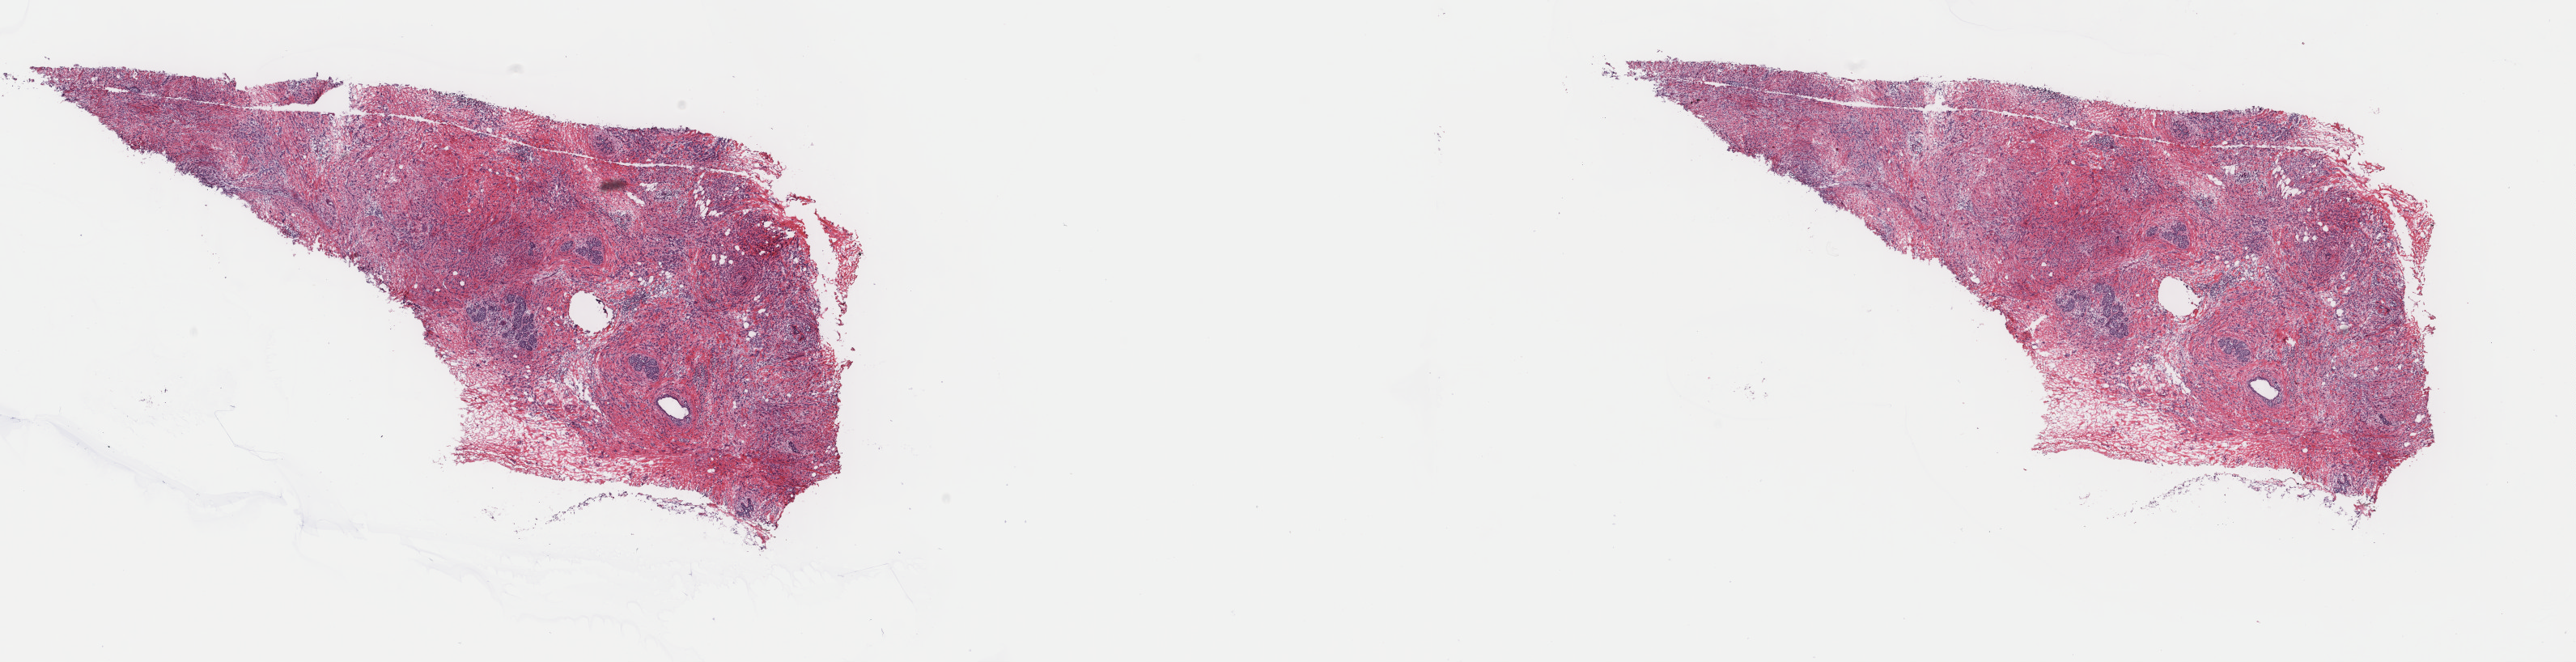
Digitized Hematoxylin and eosin (H&E) stained tissue section (whole slide) — a low-resolution overview of the entire scanned area, about 25.3 x 6.5 mm. Frozen section from the top of the tissue portion. Breast, primary tumour sample. Patient: female, age at initial diagnosis 44 years. Slide review estimates, as recorded: tumour cells 90%, tumour nuclei 80%, normal cells 5%, stromal cells 5%, necrosis 0%. Infiltration values recorded for this section: lymphocyte infiltration 0%, monocyte infiltration 0%, neutrophil infiltration 0%.
Diagnosis: Lobular carcinoma, NOS. Laterality: right. AJCC pathologic stage: IIB (7th edition).